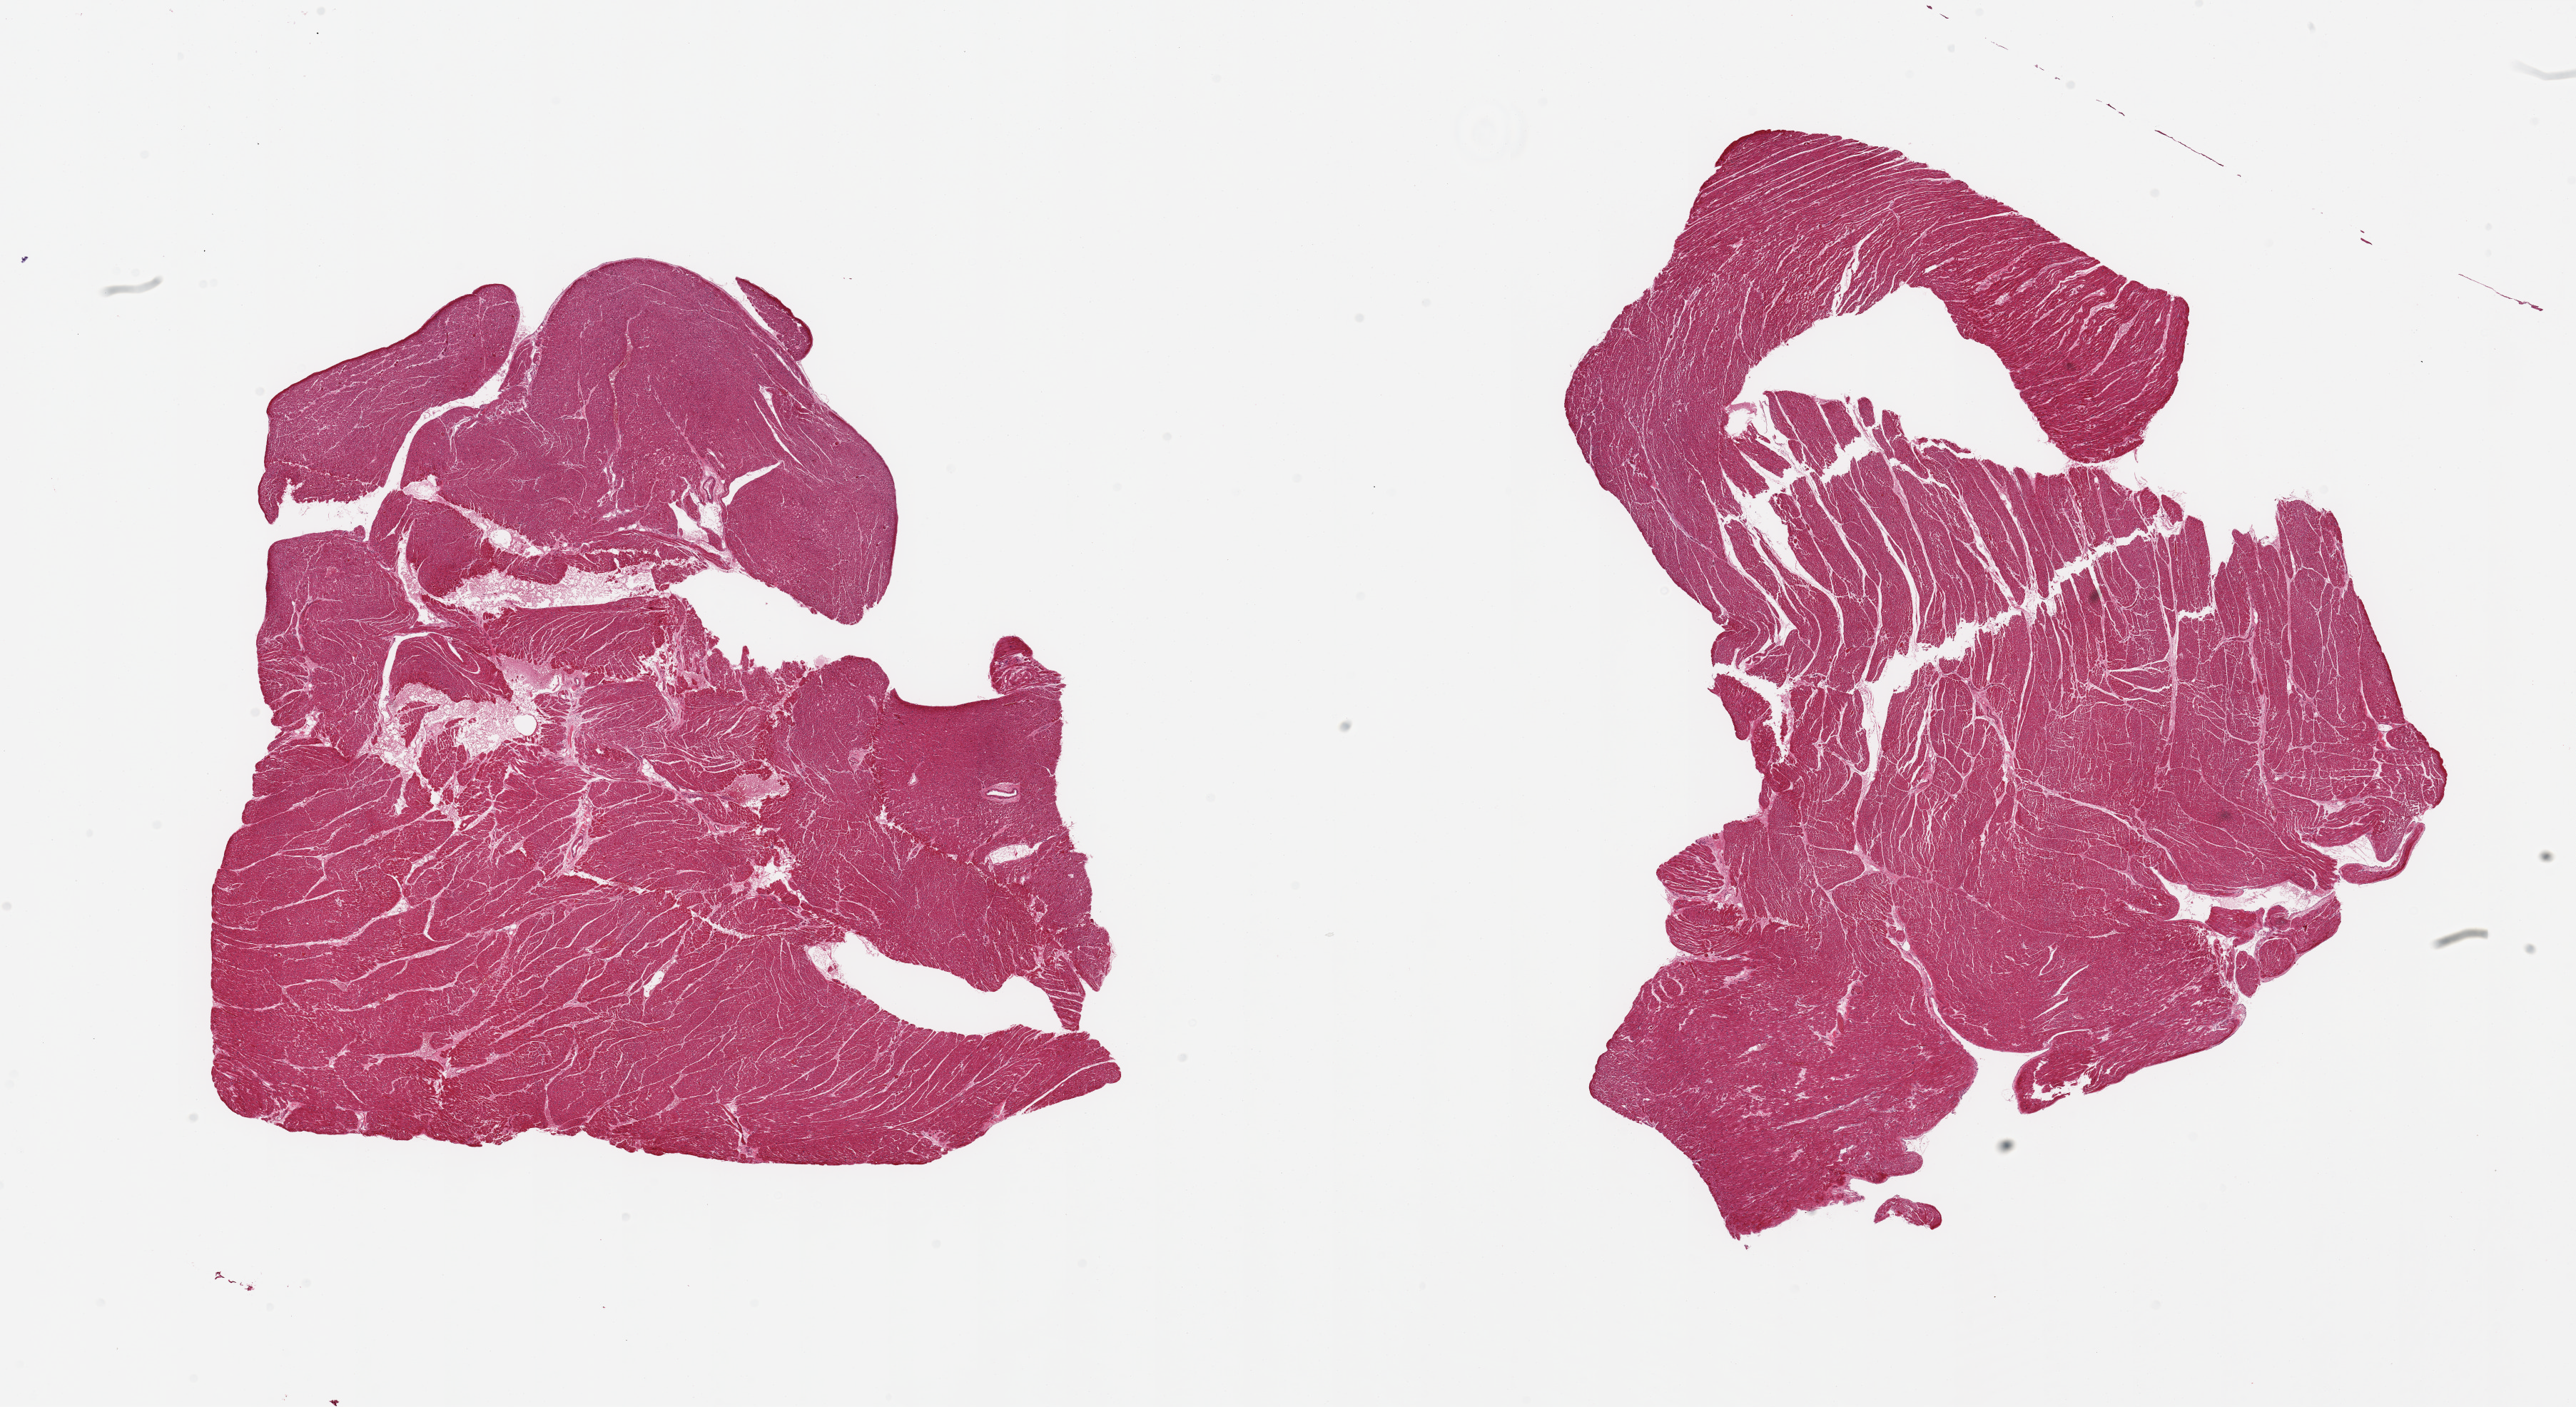
Digitized hematoxylin and eosin (H&E)-stained section, brightfield — whole scanned area (about 28.5 x 15.6 mm) shown as a low-resolution overview. PAXgene-fixed, paraffin-embedded tissue. Sampled site (target tissue): heart. Tissue donor sample.
Reviewer comment on this tissue sample: 2 pieces; enlarged nuclei consistent with hypertrophy.